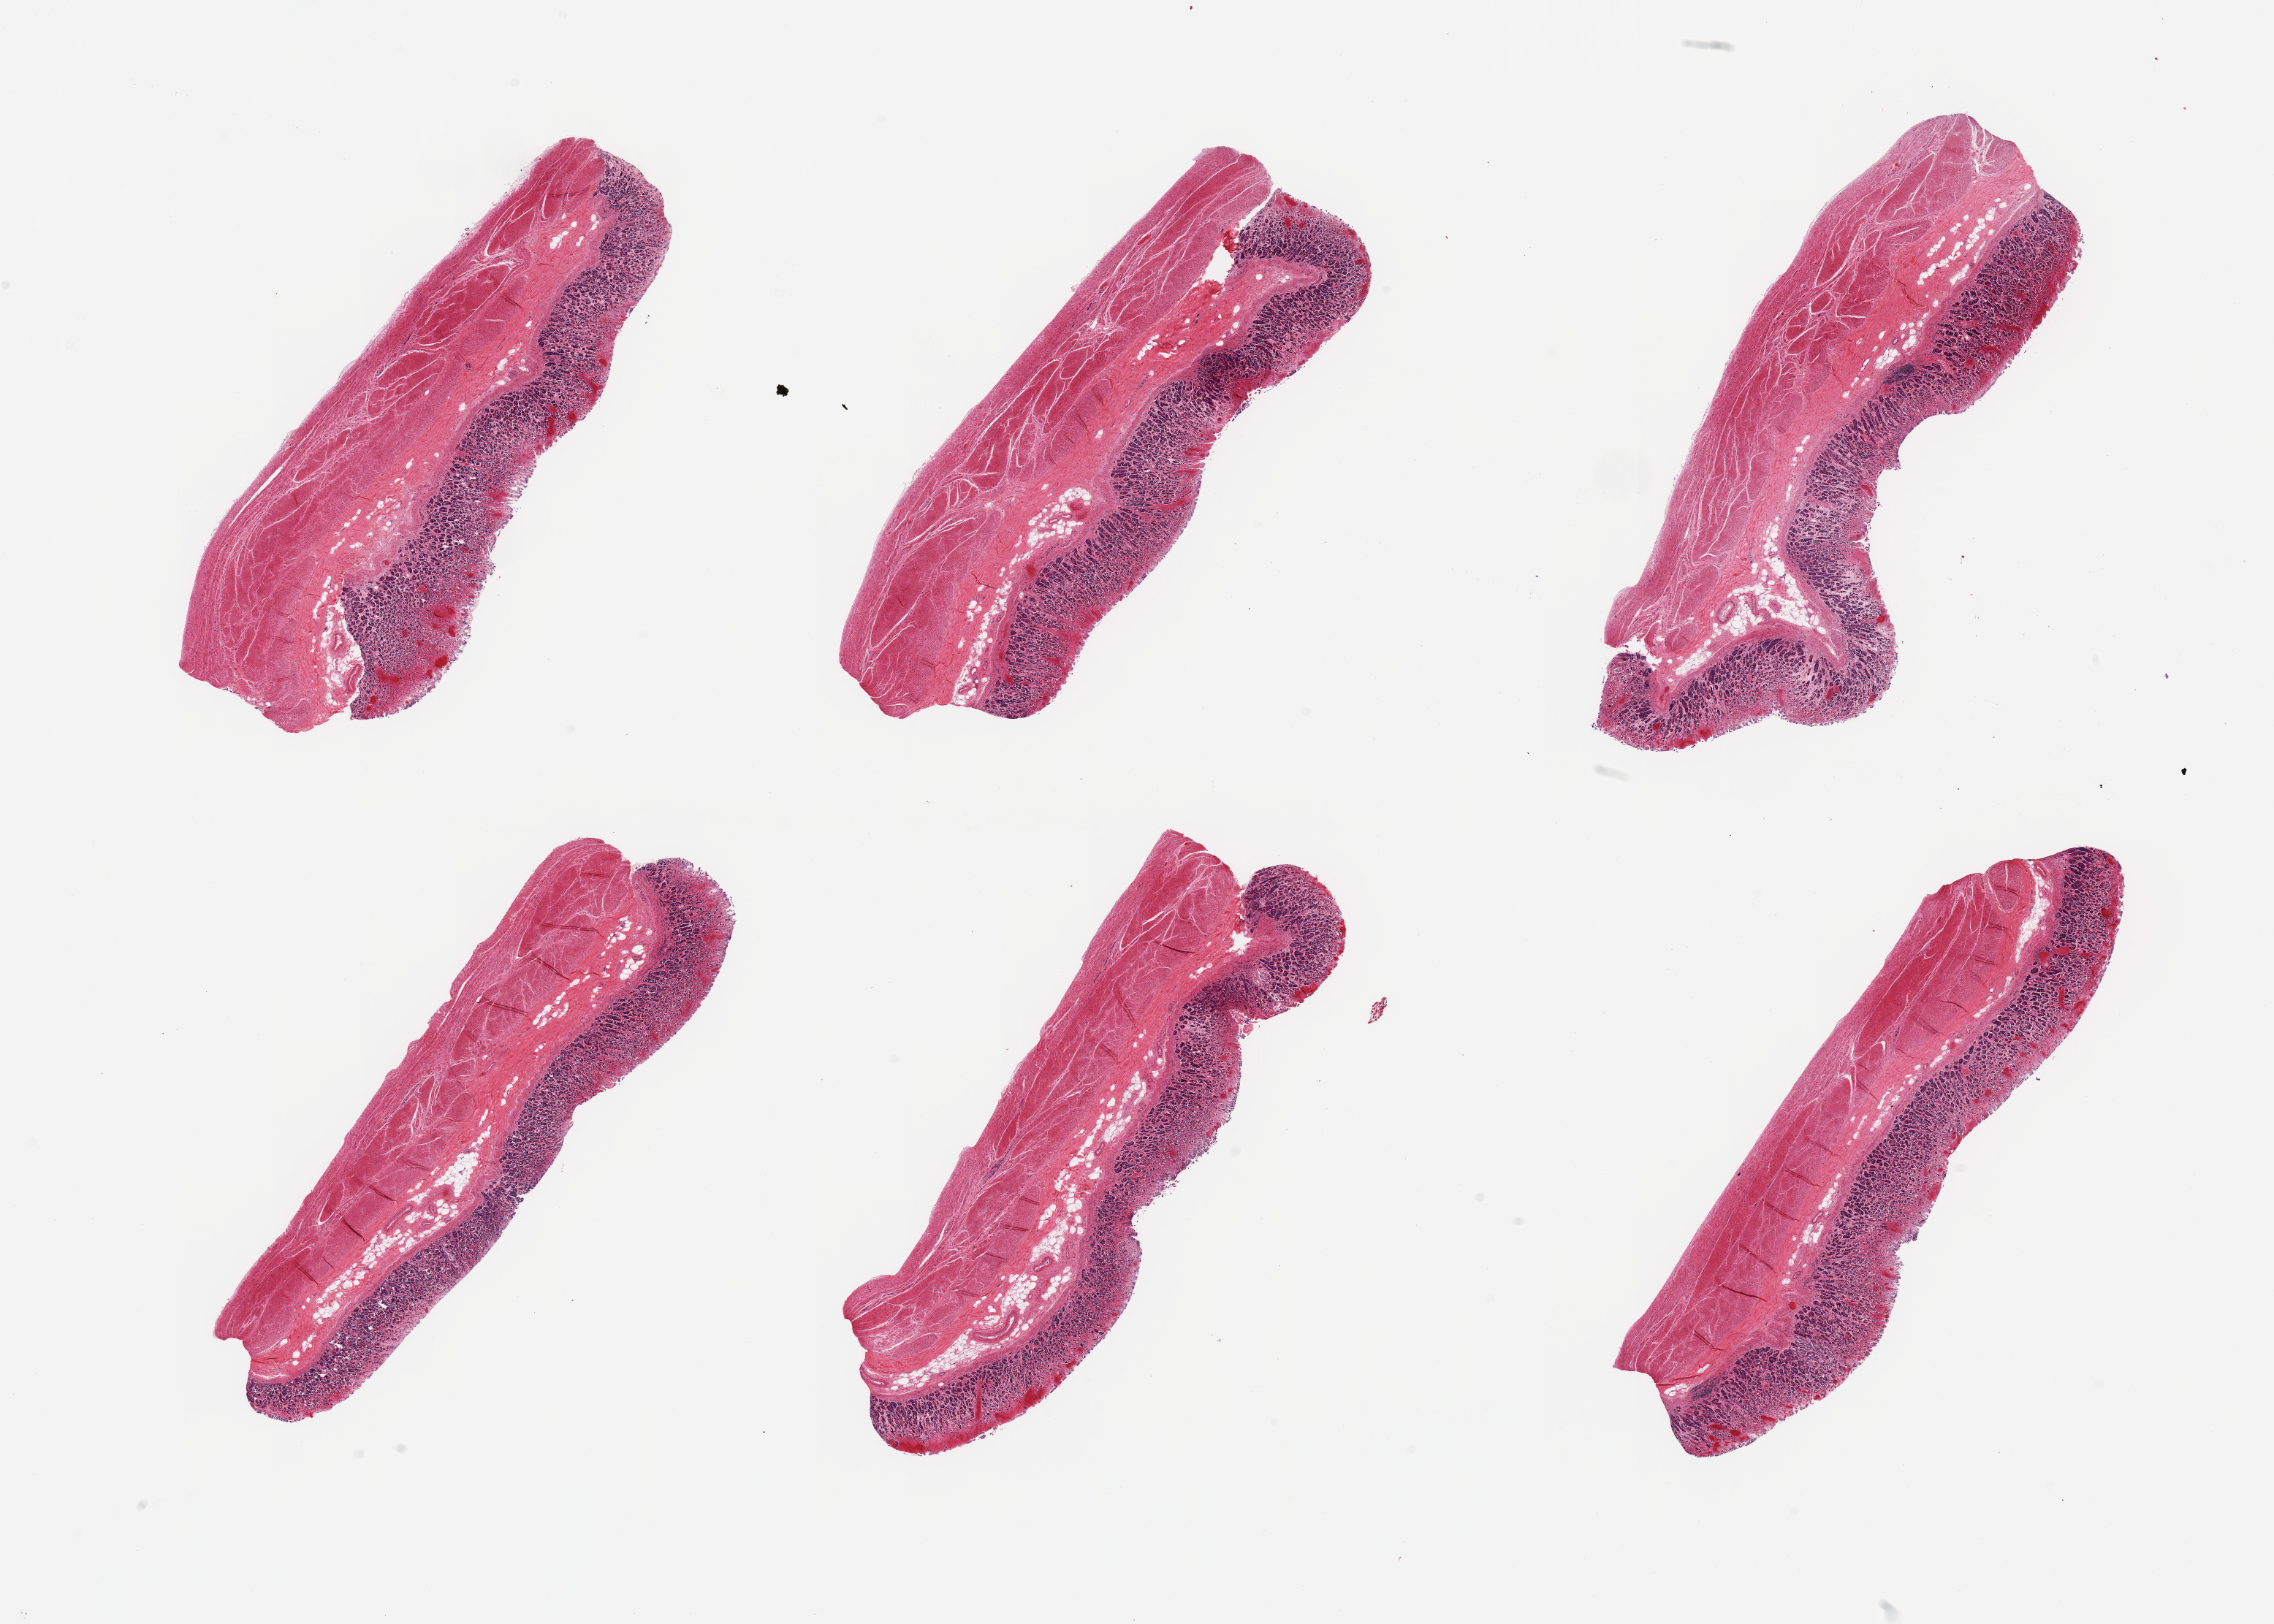
Haematoxylin and eosin whole-slide image — whole scanned area (about 24.6 x 17.6 mm, acquisition: 20x scan) shown as a low-resolution overview; PAXgene-fixed paraffin-embedded (PFPE) section; sampled site (target tissue): stomach; tissue donor sample. Male donor.
Pathologist's review note for this sample: 6 pieces, mucosa up to ~1mm but moderately-badly autolyzed.